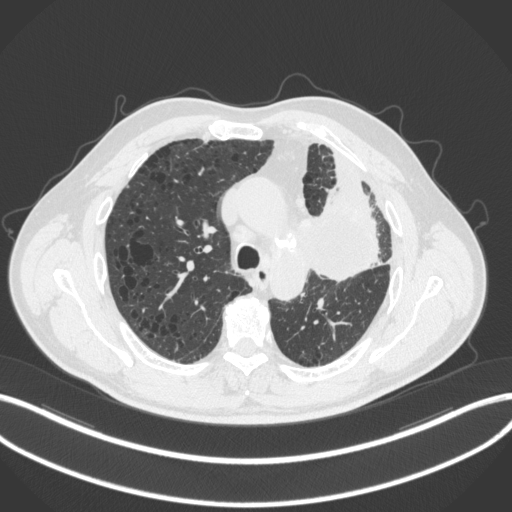
Chest CT, one axial slice. Slice 204 of 286 in the series (ordered by position). 120 kVp. Lung window (W 1500 / L -600 HU). 1 mm slice thickness. 512 × 512 image matrix, field of view 400 × 400 mm. Patient: male, 68 years. Case-level facts recorded for this patient, not image findings: clinical TNM (as recorded): T3 N3 M1.
Outlined on this slice (rectangle marked by the reading radiologist):
- lung tumour (recorded histology: adenocarcinoma): bounding box <316,177,383,286> (left, top, right, bottom; pixels)